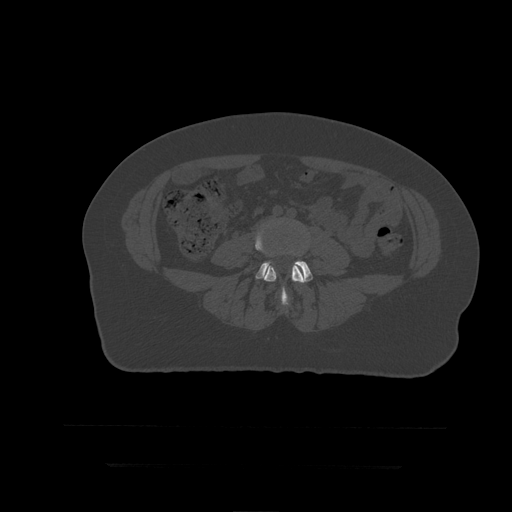
CT including the spine, one axial slice; position 86 of 399 along the scan axis; reconstruction kernel STANDARD; 120 kVp; bone window (W 1800 / L 400 HU); 1.25 mm slice thickness; 512 × 512 image matrix, field of view 450 × 450 mm. Patient age 41 years. From the clinical record (not read from this slice): primary cancer: breast.
Structures marked on this image (semi-automatically segmented with operator editing):
- L4 vertebra: box from (x=256, y=218) to (x=306, y=305) px
- L5 vertebra: (x=256, y=251)–(x=313, y=282)